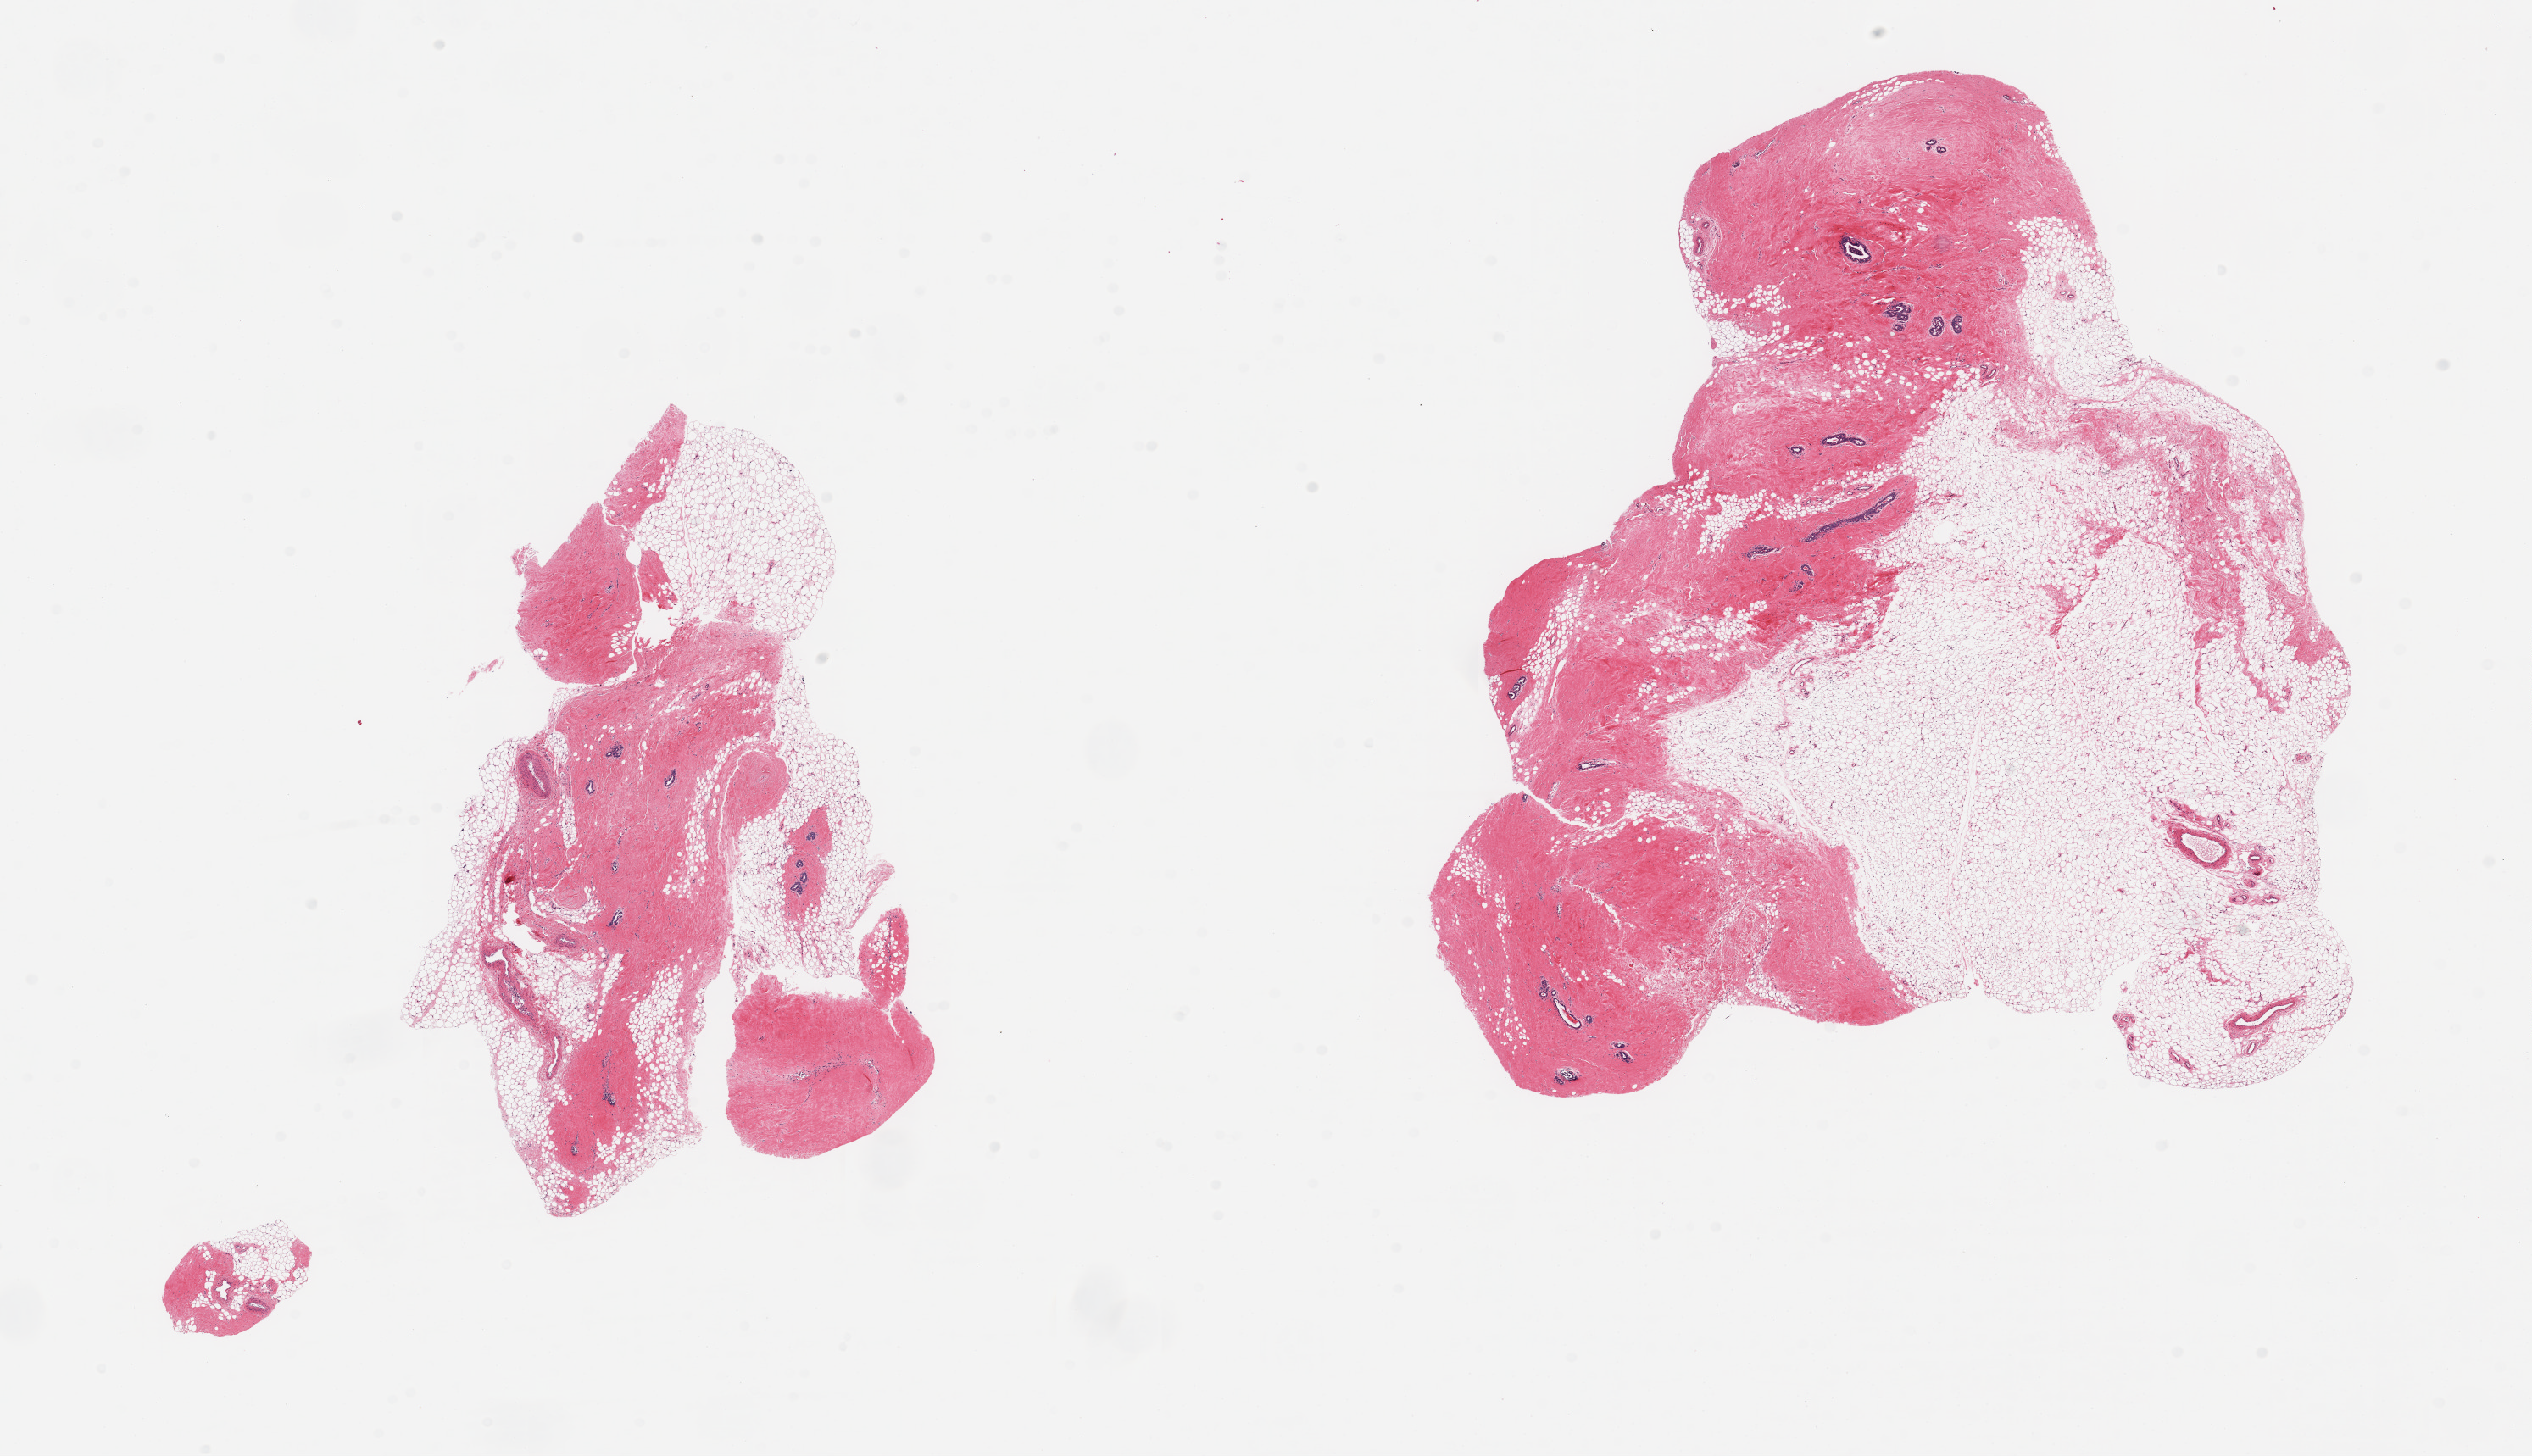
Haematoxylin and eosin whole-slide image, a low-resolution overview of the entire scanned area, about 23.6 x 13.6 mm (slide scanned at 20x). PAXgene-fixed, paraffin-embedded tissue. Target tissue: breast. Donor tissue sample. Male donor.
• pathologist's review note for this sample: 2 pieces; gynecomastoid changes